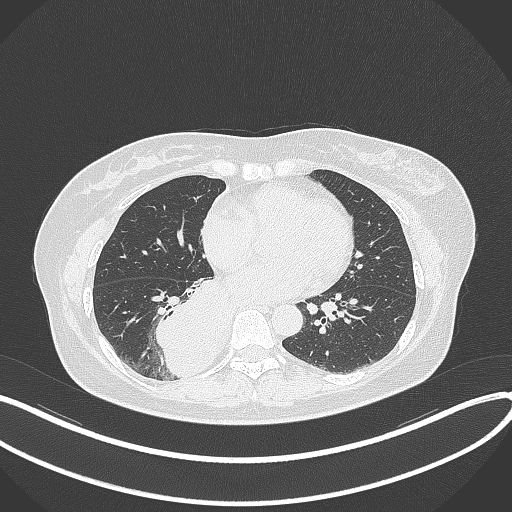
Chest CT, one axial slice; position 147 of 331 along the scan axis; 120 kVp; lung window (W 1500 / L -600 HU); 1 mm slice thickness; 512 × 512 image matrix, field of view 400 × 400 mm. Patient: female, 54 years. From the clinical record (not read from this slice): clinical TNM (as recorded): T4 N0 M0.
Outlined on this slice (rectangle marked by the reading radiologist):
- lung tumour (recorded histology: adenocarcinoma): box from (x=156, y=273) to (x=232, y=382) px